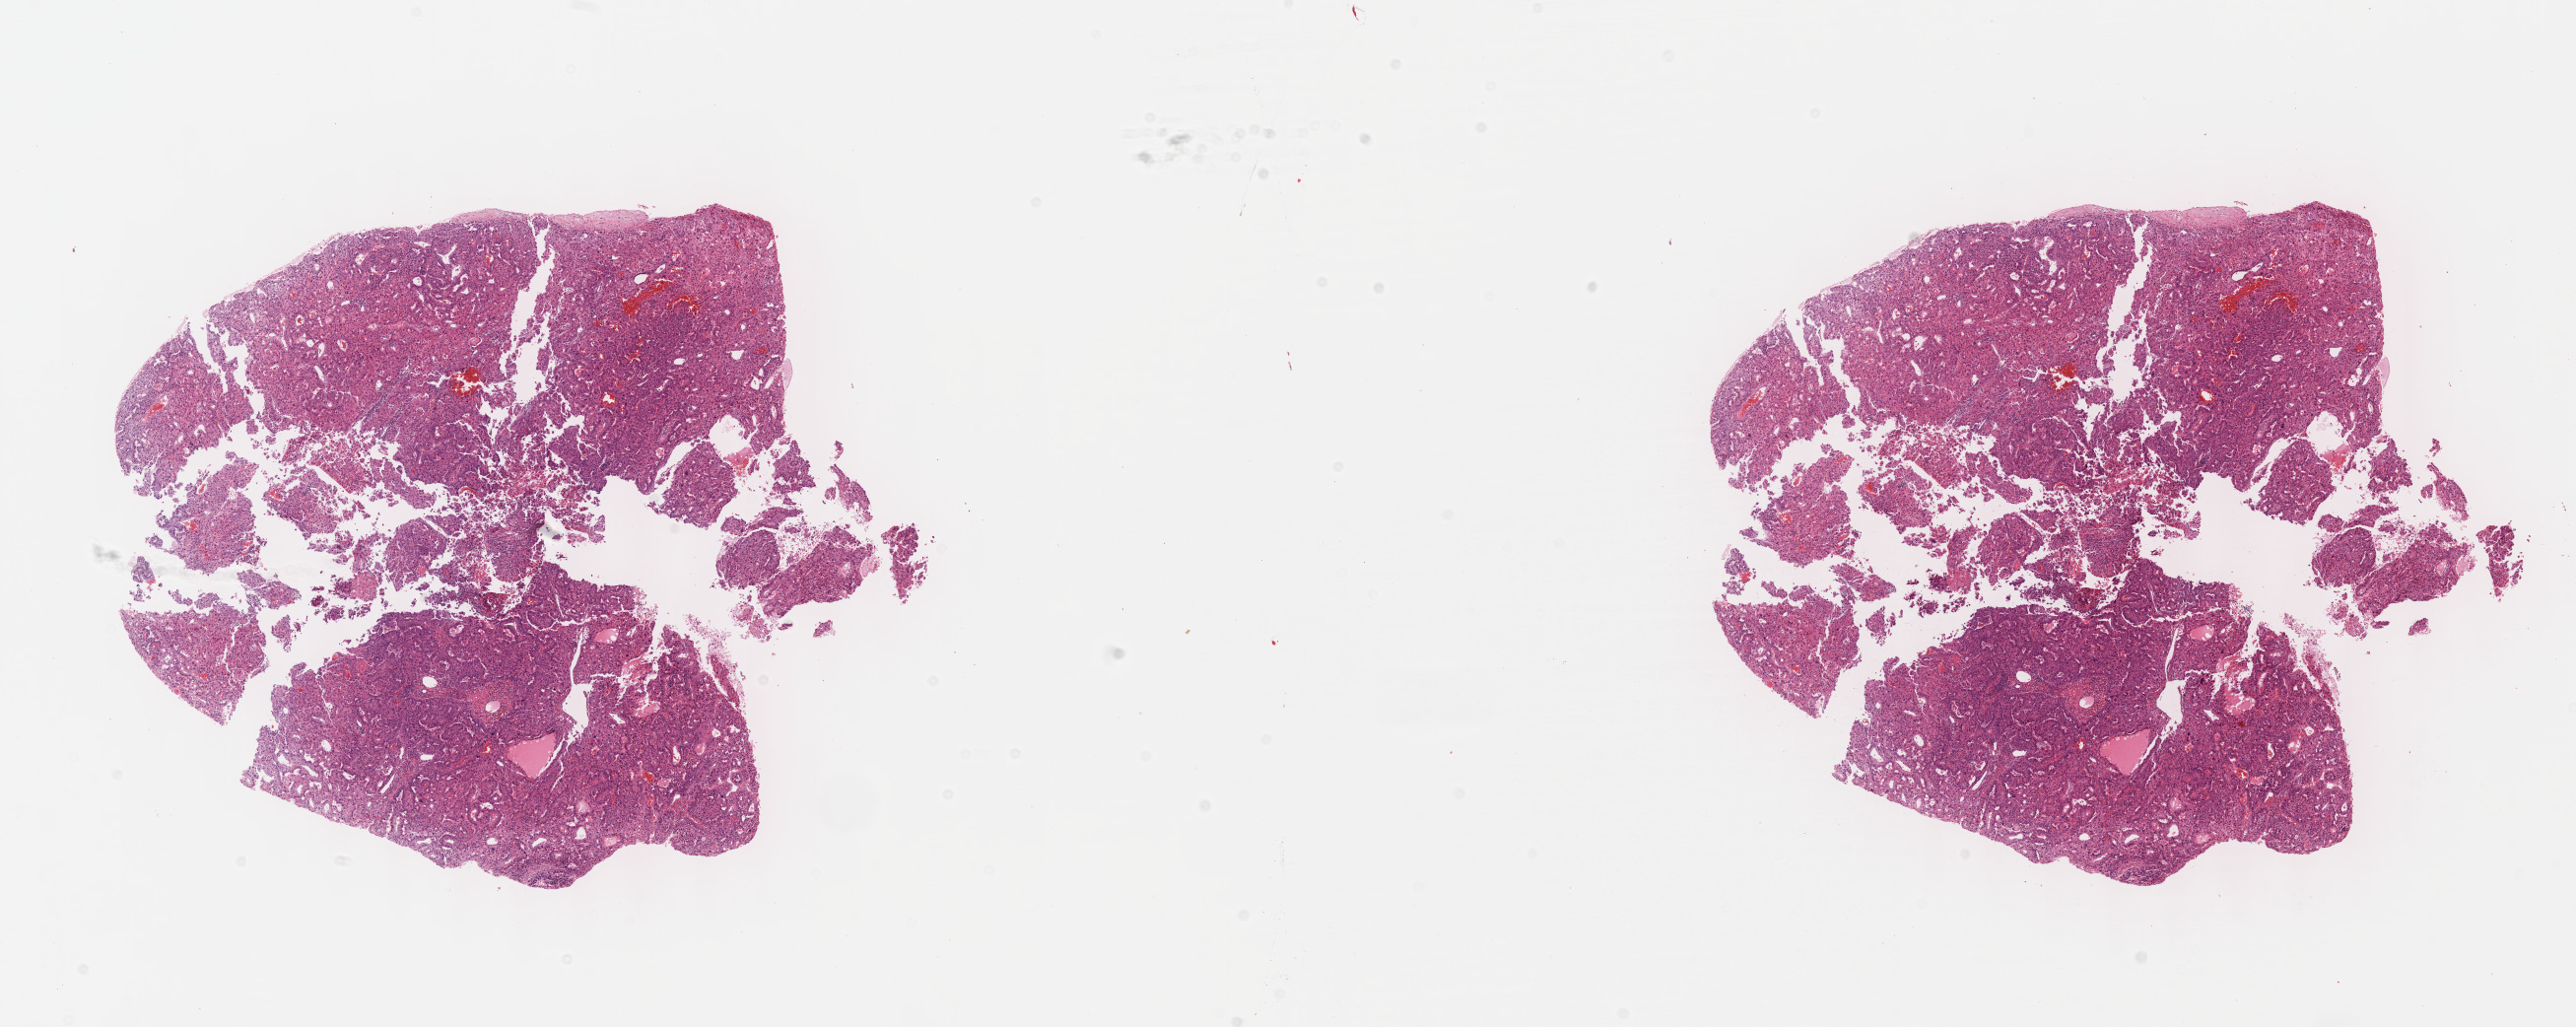
H&E-stained whole-slide image, whole scanned area (about 21.1 x 8.4 mm) shown as a low-resolution overview, formalin-fixed paraffin-embedded (FFPE) diagnostic section, liver, primary tumour sample. Male, age 55 years at initial diagnosis. Histologic grade: G3 (poorly differentiated).
AJCC pathologic stage: I. Diagnosis: Hepatocellular carcinoma, NOS. TNM: T1 N0 M0.